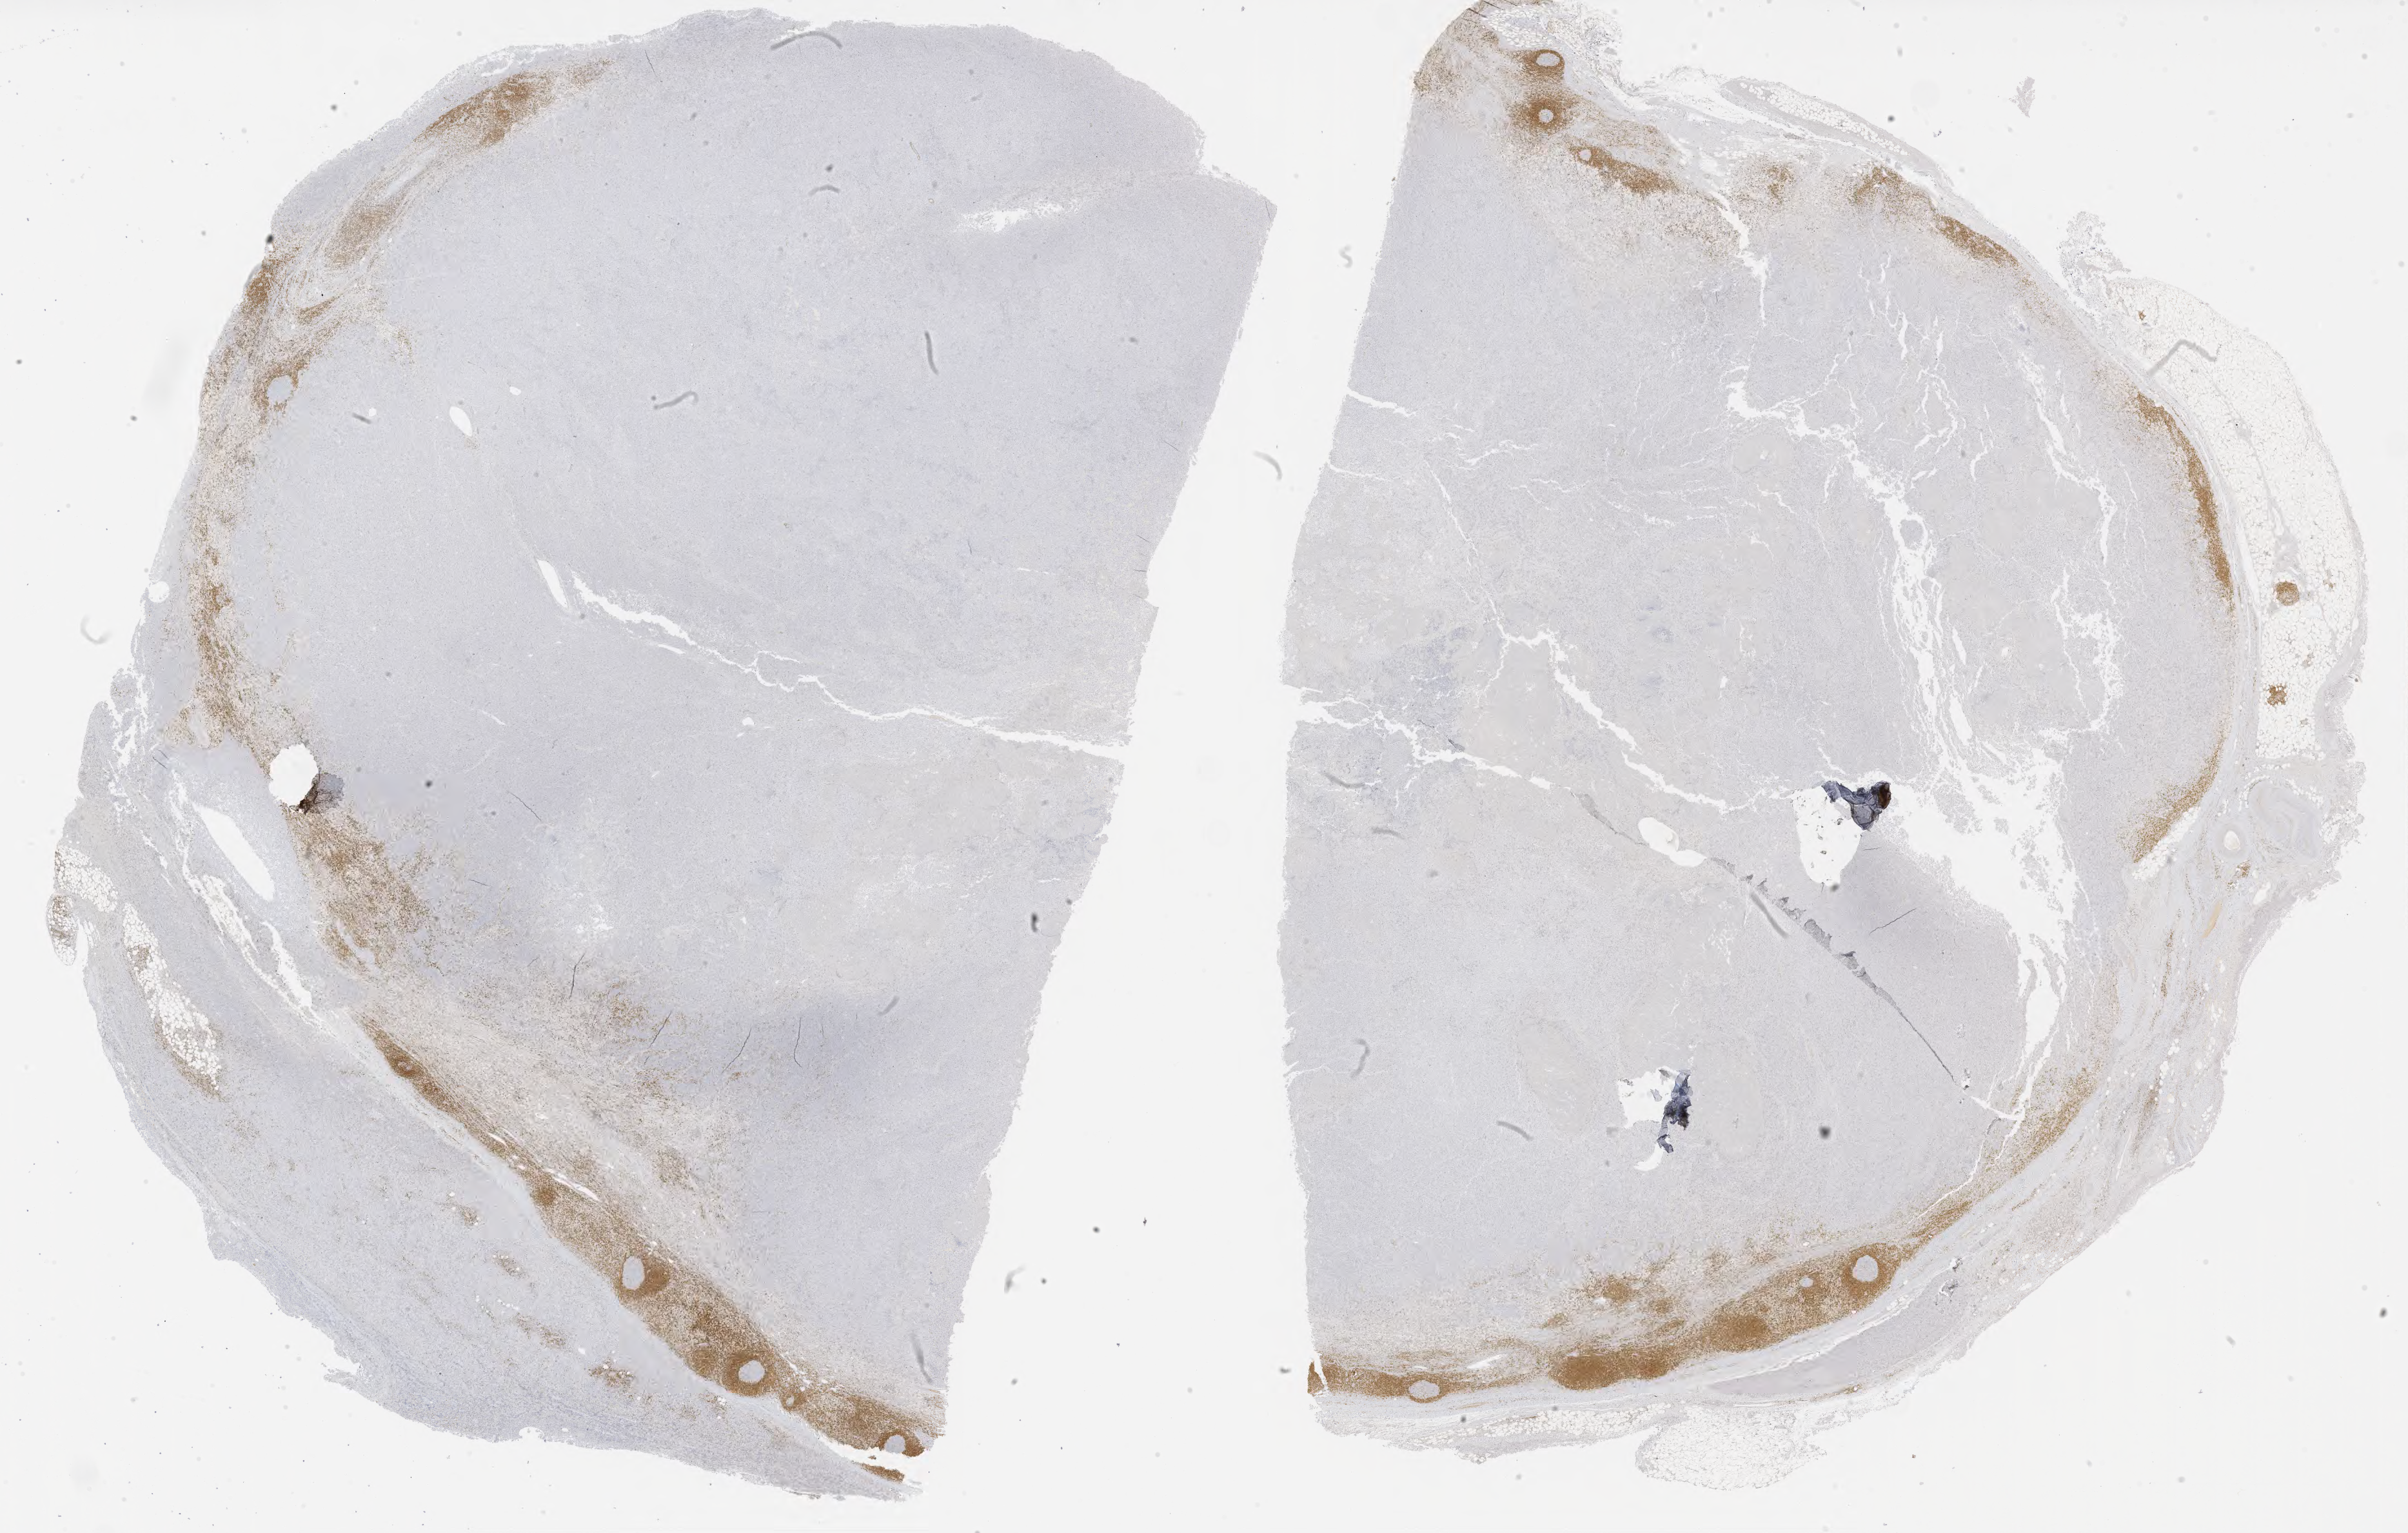
IHC for BCL2, whole-slide image — a low-resolution overview of the entire scanned area, about 30.2 x 19.2 mm, tumor tissue. Male patient, aged 48.
Diagnosis: Burkitt lymphoma, NOS.